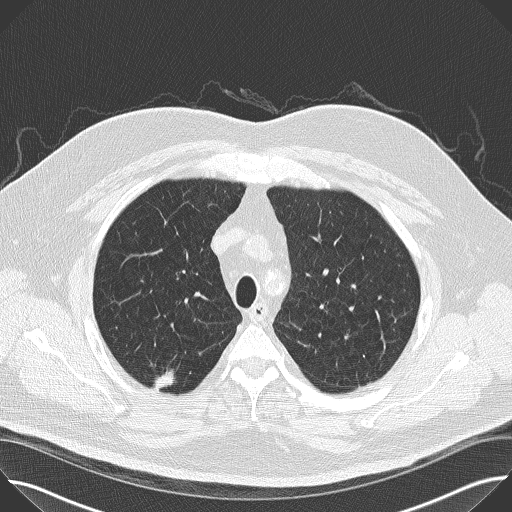
Low-dose screening chest CT, axial slice. First (baseline) screen. Lung window (W 1500 / L -600 HU). Slice 125 of 160 in the series. Male, age 65 years at enrolment.
- Lesion marked by an expert reader, bounding box (x1, y1, x2, y2) in pixels: (140, 365, 189, 404).
- The screening reader recorded 2 non-calcified nodules or masses ≥4 mm on this exam (right upper lobe, right upper lobe); which of them this box marks is not recorded.
- Official screen result: positive, change unspecified: nodule(s) >= 4 mm or enlarging nodule(s), mass(es), or other non-specific abnormalities suspicious for lung cancer.